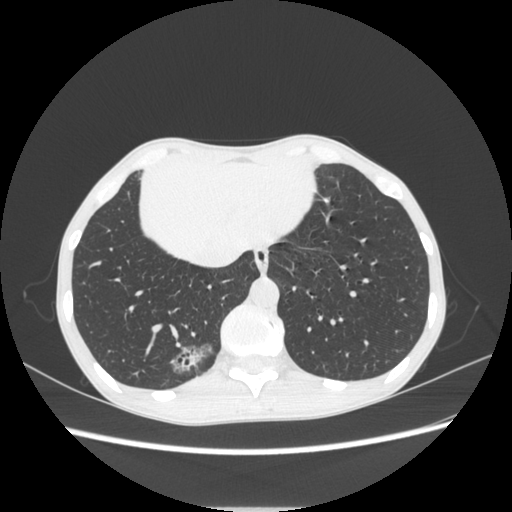
Chest CT, one axial slice; position 68 of 272 along the scan axis; 120 kVp; lung window (W 1500 / L -600 HU); 512 × 512 image matrix, field of view 350 × 350 mm. Patient: female, 51 years. From the clinical record (not read from this slice): clinical TNM (as recorded): T1c N0 M0; histopathological grade: G2-3.
Outlined on this slice (rectangle marked by the reading radiologist):
- lung tumour (recorded histology: adenocarcinoma): box from (x=166, y=330) to (x=223, y=392) px